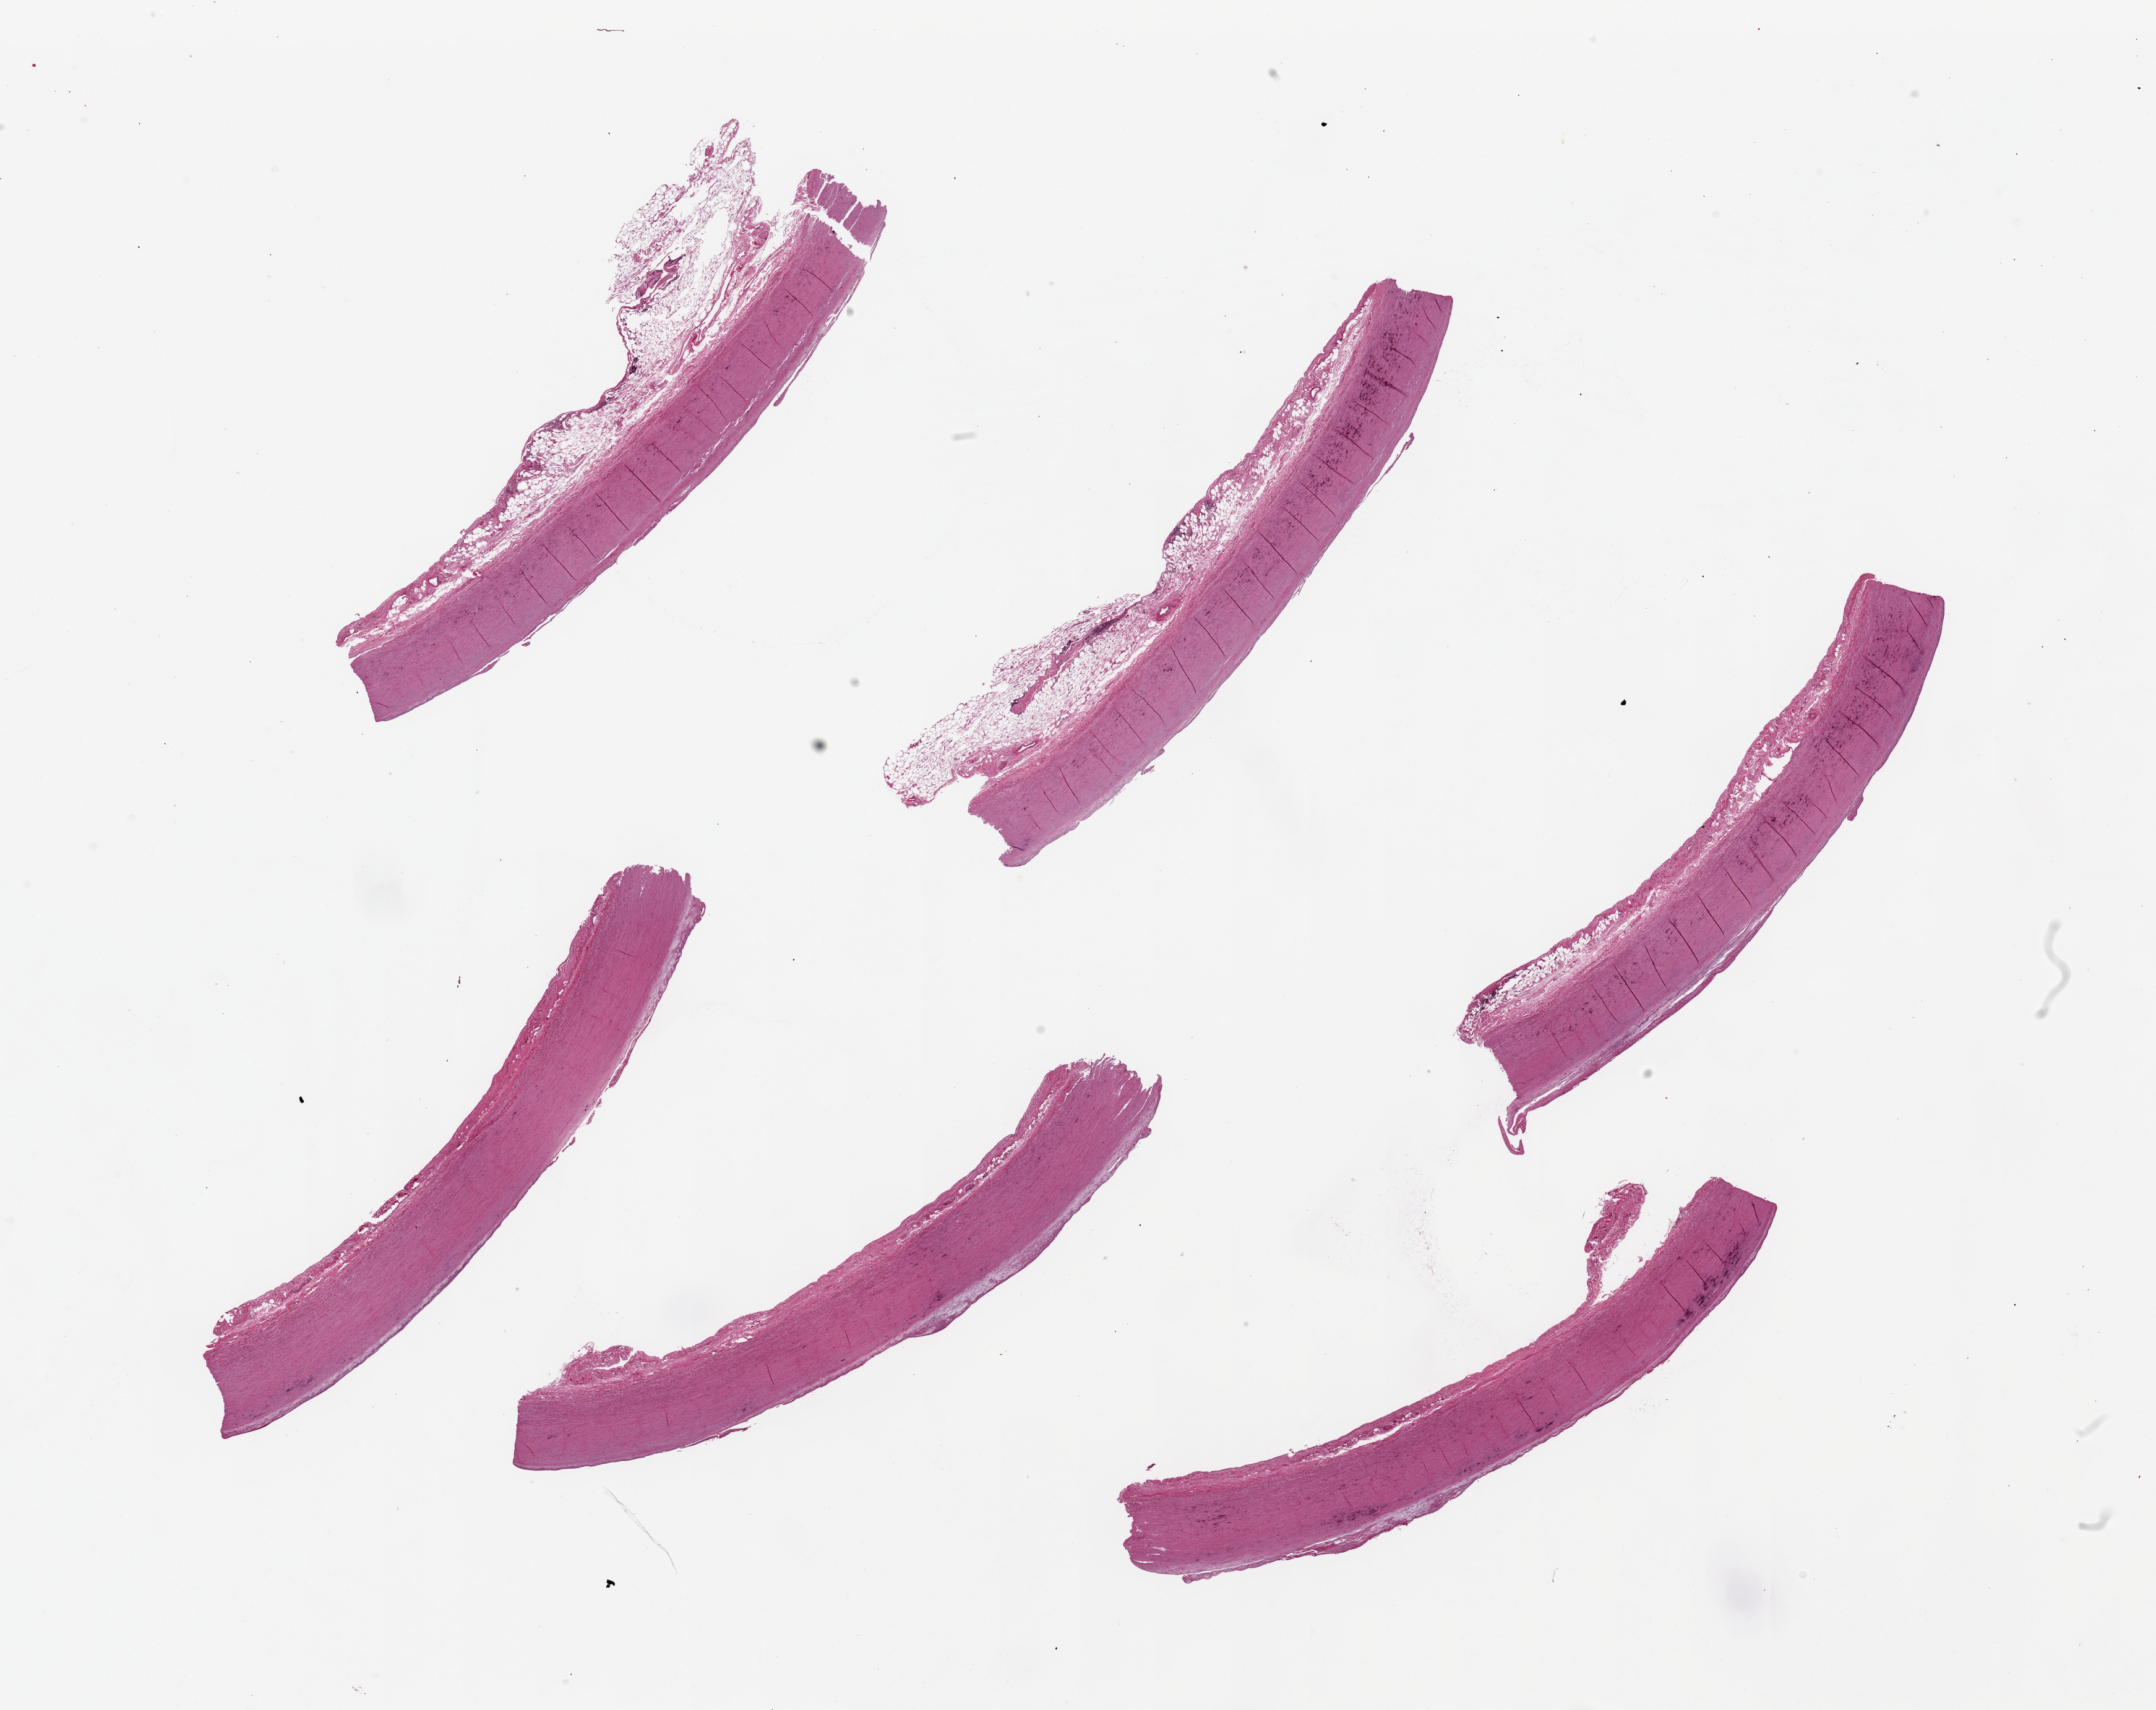
H&E whole-slide image, brightfield, a low-resolution overview of the entire scanned area, about 27.6 x 21.9 mm, PAXgene-fixed paraffin-embedded (PFPE) section, target tissue: aorta, donor tissue sample. Donor sex: female.
Pathologist's review note for this sample: 6 pieces, up to 10x2mm; up to 1.8 mm adventitial adipose in 3 pieces.